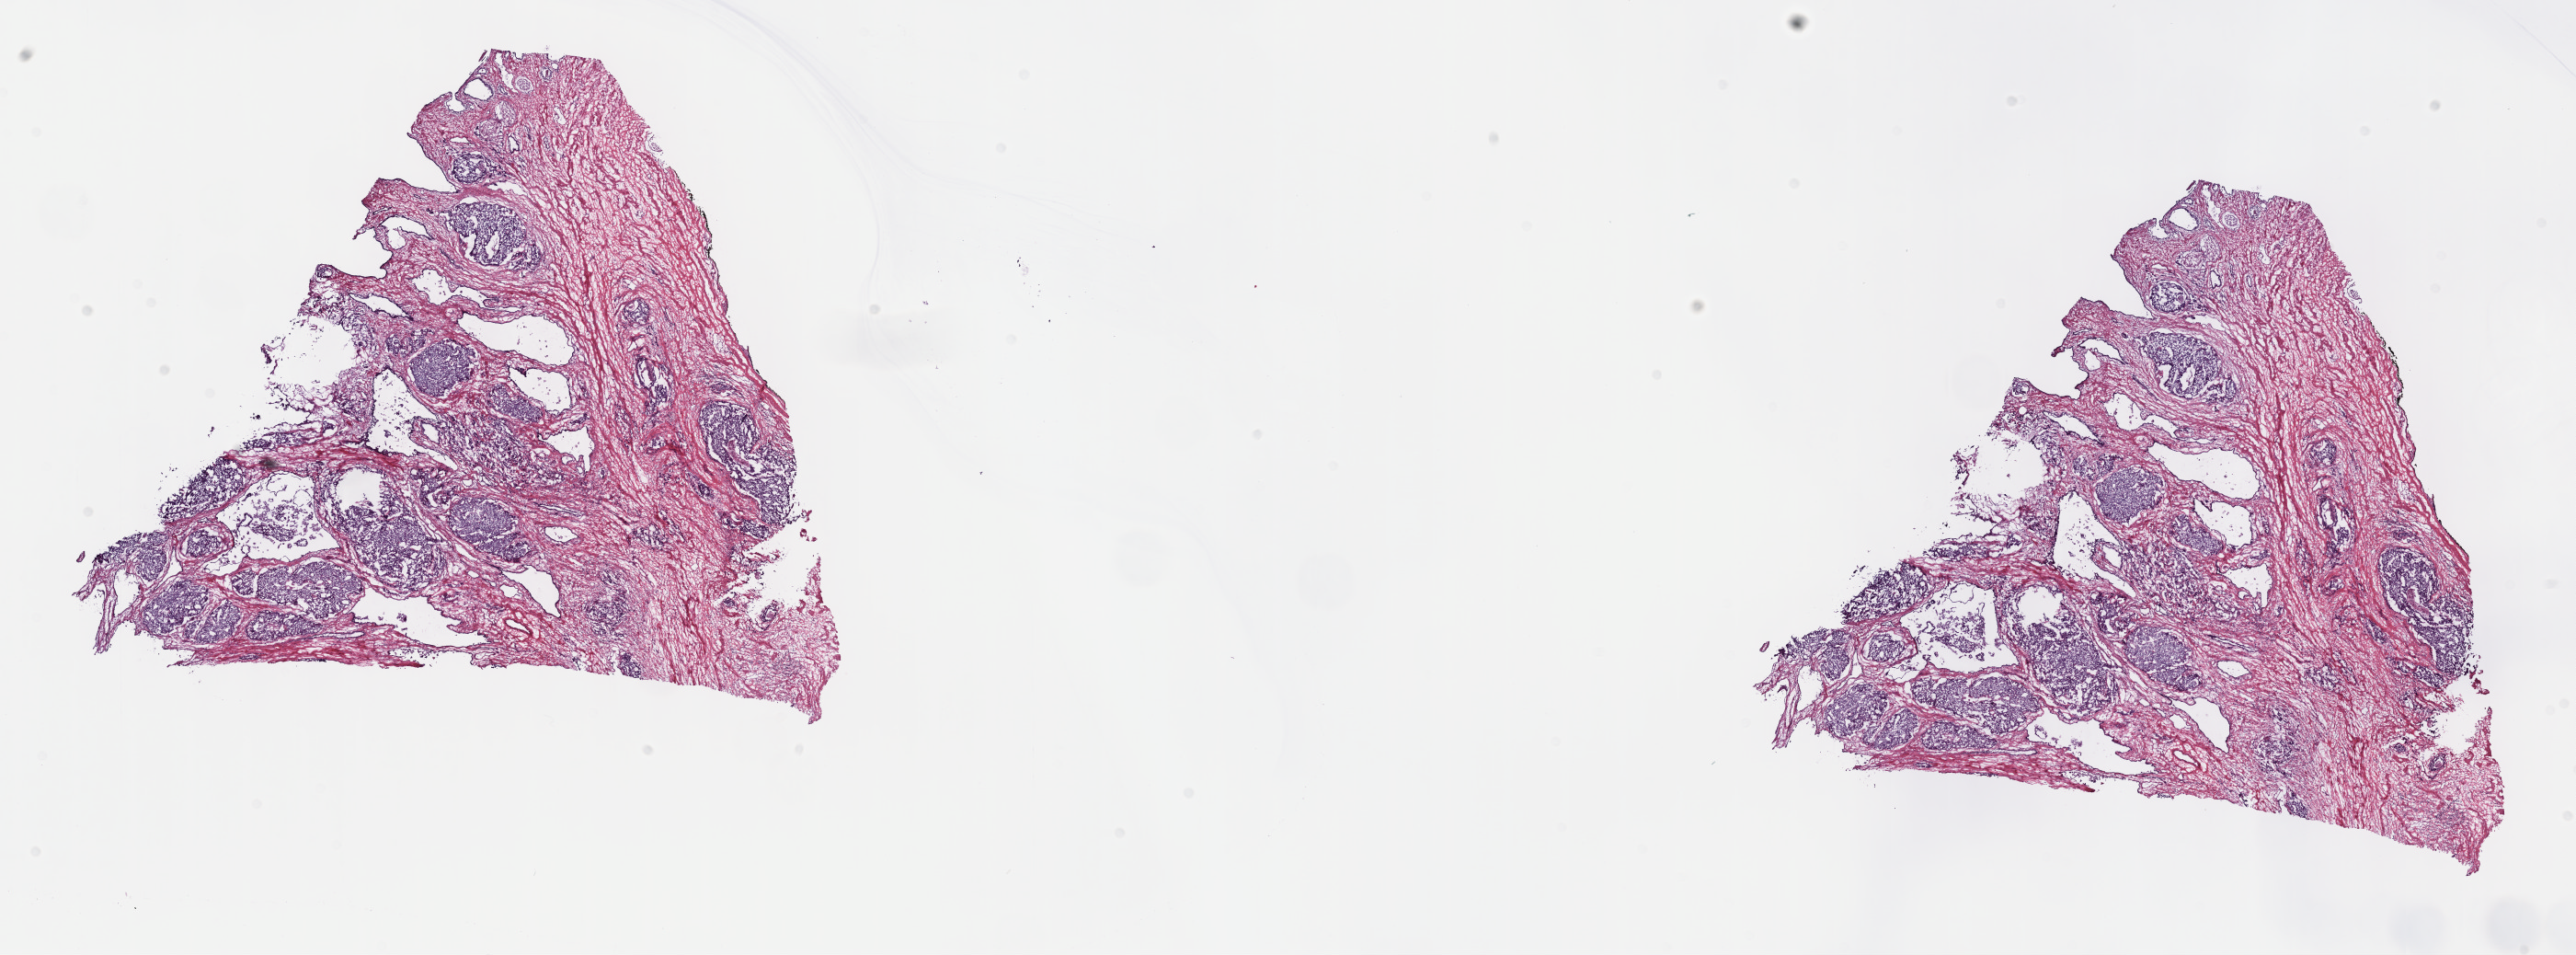
Digitized Hematoxylin and eosin (H&E) stained tissue section (whole slide) — low-resolution overview of the scanned area, about 22.7 x 8.4 mm (acquisition: 40x scan); frozen section from the top of the tissue portion; prostate, primary tumour sample. Patient: male, age at initial diagnosis 64 years. Gleason score: 9 (4+5). Slide review estimates, as recorded: tumour cells 30%, tumour nuclei 60%, normal cells 10%, stromal cells 60%, necrosis 0%. Inflammatory infiltration, as recorded: lymphocyte infiltration 0%, monocyte infiltration 0%, neutrophil infiltration 0%.
Laterality: bilateral. Pathologic diagnosis: Adenocarcinoma, NOS (prostate gland).